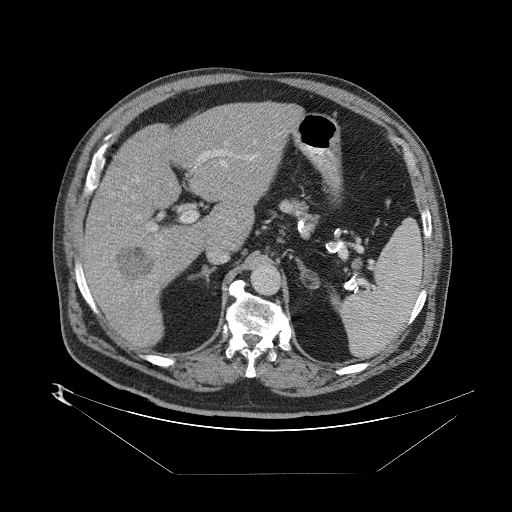
Contrast-enhanced abdominal CT (liver protocol), one axial slice. Slice 48 of 89 in the series (ordered by position). Reconstruction kernel STANDARD. 140 kVp. One of 2 acquisitions stored at this slice position. Soft-tissue window (W 400 / L 40 HU). 2.5 mm slice thickness. 512 × 512 image matrix, field of view 480 × 480 mm. From the clinical record (not read from this slice): diagnosis: hepatocellular carcinoma (patient treated with transarterial chemoembolisation; whether this scan precedes or follows treatment is not stated here); TNM stage (as recorded): Stage-II; Child-Pugh class: B; tumour differentiation: moderately differentiated; tumour nodularity: multinodular.
Structures marked on this image (semi-automatic segmentation, software-assisted and operator-edited):
- abdominal aorta: bounding box <252,264,280,293> (left, top, right, bottom; pixels)
- liver parenchyma outside the tumour (the mass and vessels are separate outlines, so this box may not span the whole liver): <82,99,300,348>
- mass: <111,237,155,282>
- liver vessels: <84,112,298,312>